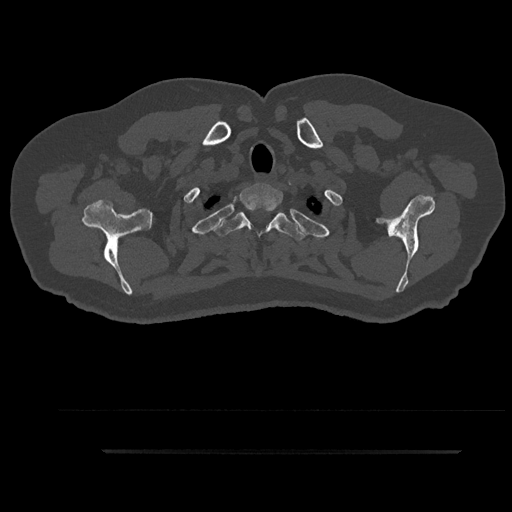
CT including the spine, one axial slice; reconstruction kernel Br40s/3; bone window (W 1800 / L 400 HU); 0.5 mm slice thickness; 512 × 512 image matrix, field of view 432 × 432 mm. Patient: male, 63 years. Case-level facts recorded for this patient, not image findings: primary cancer: renal.
Structures marked on this image (semi-automatic segmentation, software-assisted and operator-edited):
- T1 vertebra: box from (x=239, y=185) to (x=283, y=211) px
- T2 vertebra: (x=212, y=209)–(x=306, y=240)